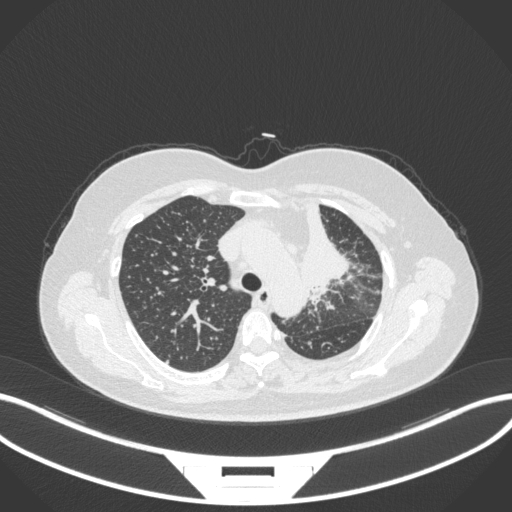
Chest CT, one axial slice. Position 244 of 348 along the scan axis. Reconstruction kernel B31f. 120 kVp. Lung window (W 1500 / L -600 HU). 512 × 512 image matrix, field of view 400 × 400 mm. Patient: female, 49 years. Case-level facts recorded for this patient, not image findings: clinical TNM (as recorded): T1c N0 M1.
Structures marked on this image (bounding box drawn by a radiologist):
- lung tumour (recorded histology: adenocarcinoma): box from (x=294, y=203) to (x=352, y=300) px